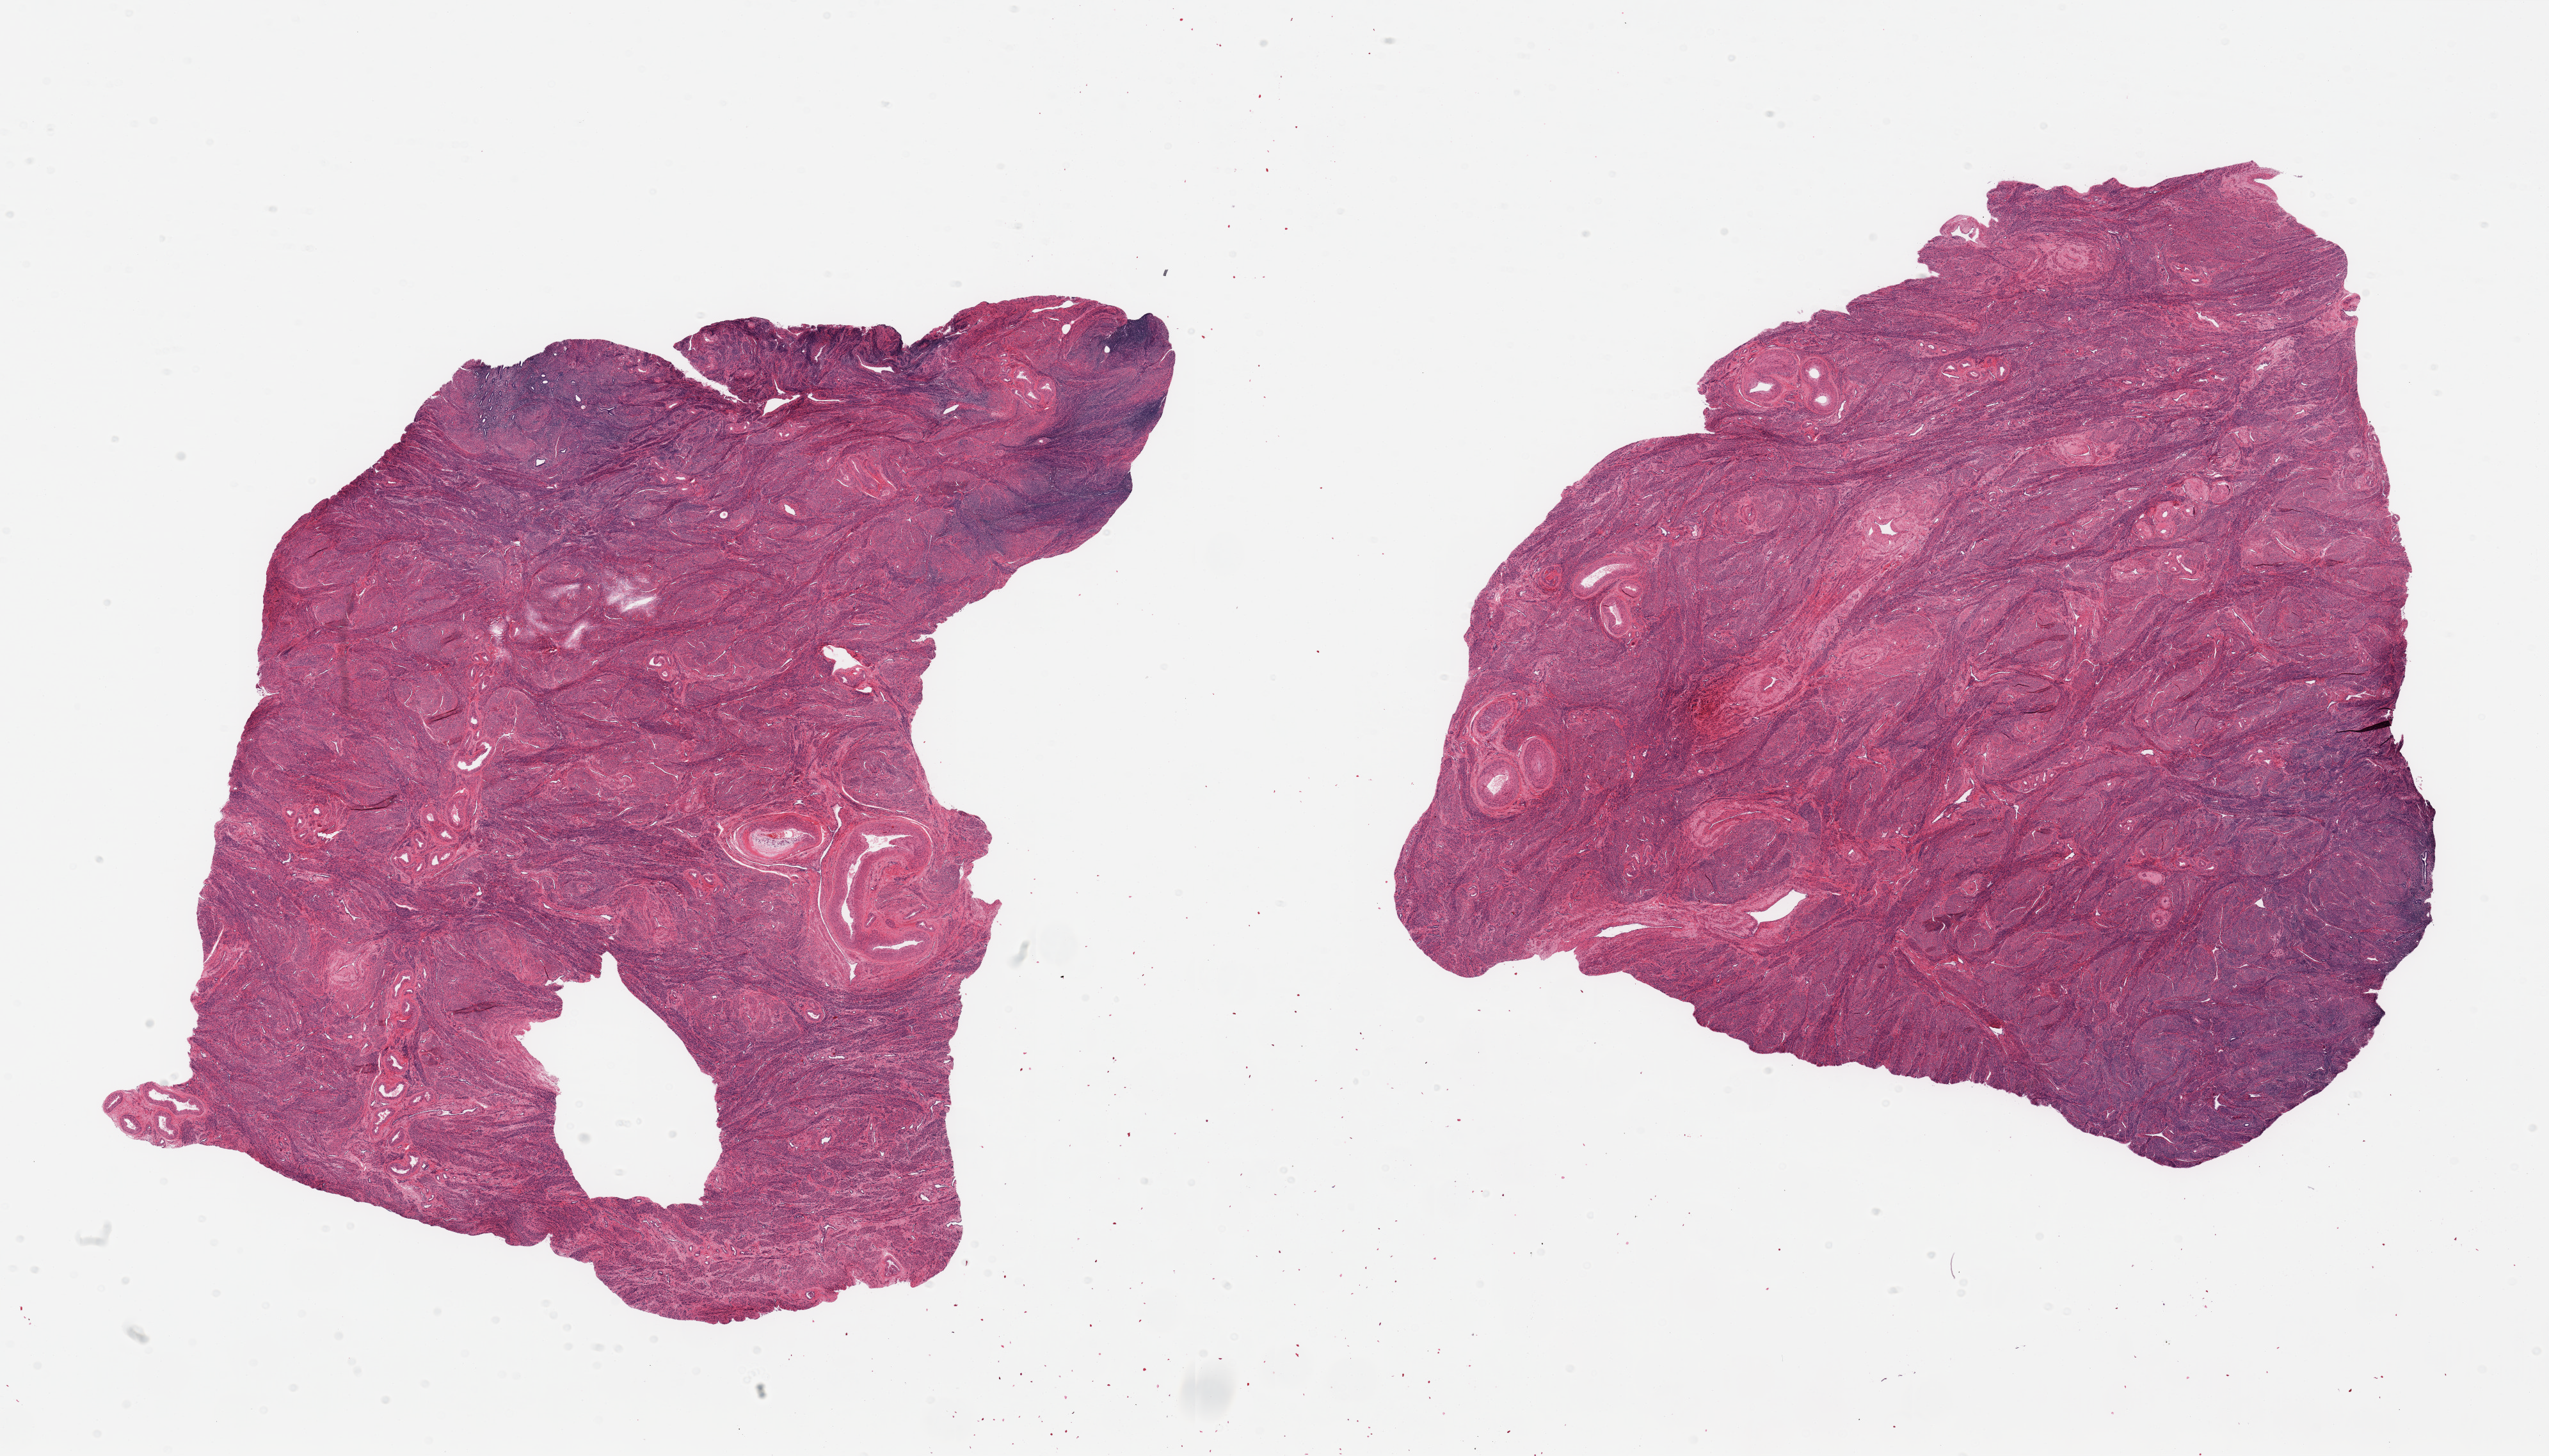
Hematoxylin and eosin (H&E) whole-slide image — low-resolution overview of the scanned area, about 31.5 x 18.0 mm; PAXgene-fixed, paraffin-embedded tissue; target tissue: uterus; donor tissue sample.
Reviewer comment on this tissue sample: 2 pieces, myometrium; Trace basalis endometrial stroma, no glandular elements.